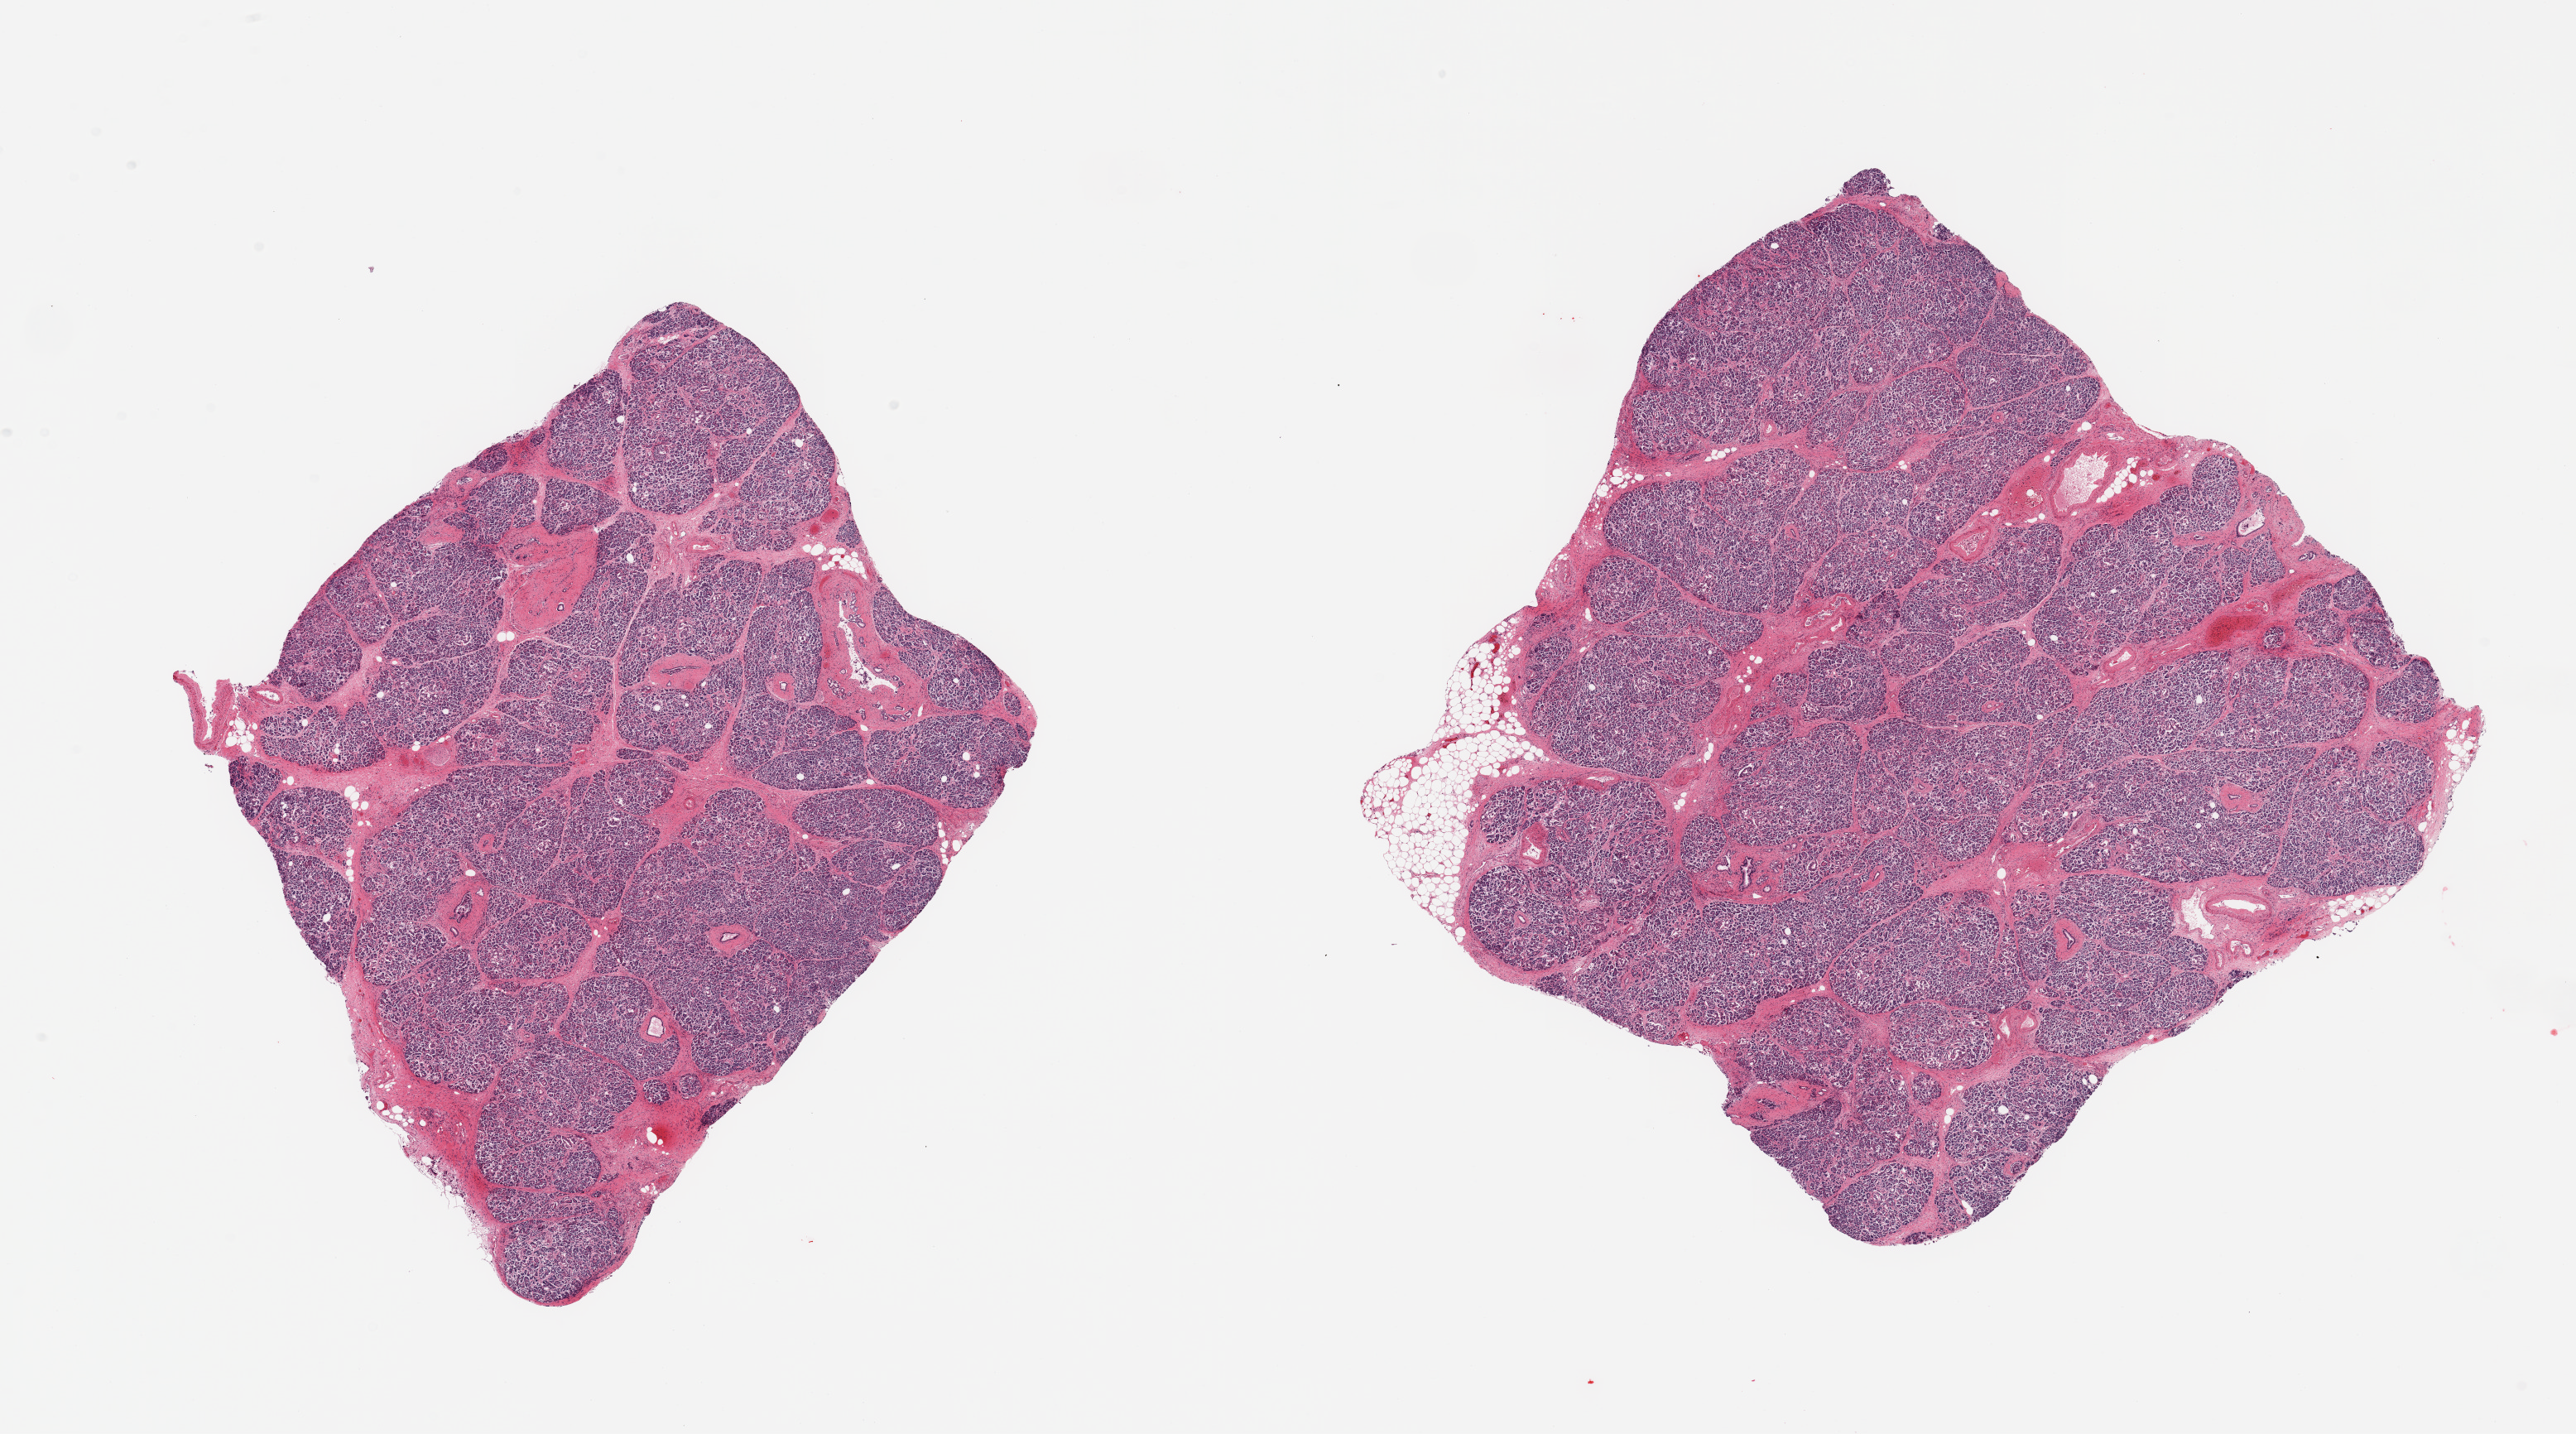
Whole-slide image, hematoxylin and eosin (H&E) stain — shown as a low-resolution overview of the whole scanned area (about 24.6 x 13.7 mm); PAXgene-fixed, paraffin-embedded tissue; section of pancreas (target tissue); tissue donor sample. Female donor.
Pathologist's review note for this sample: 2 pieces; moderate increase in fibrous tissue.